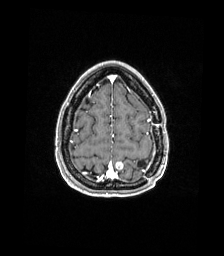
Brain MRI from a brain-tumour surgery series, one axial slice; position 40 of 176 along the scan axis; T1-weighted post-contrast; 1 mm slice thickness; 224 × 256 image matrix, field of view 224 × 256 mm. From the clinical record (not read from this slice): histopathology: Atypical meningioma; WHO grade: 2.
Outlined on this slice (manually delineated by an expert):
- previous resection cavity: bounding box (x1, y1, x2, y2) in pixels: (137, 160, 146, 169)
- tumour: (115, 161, 123, 170)